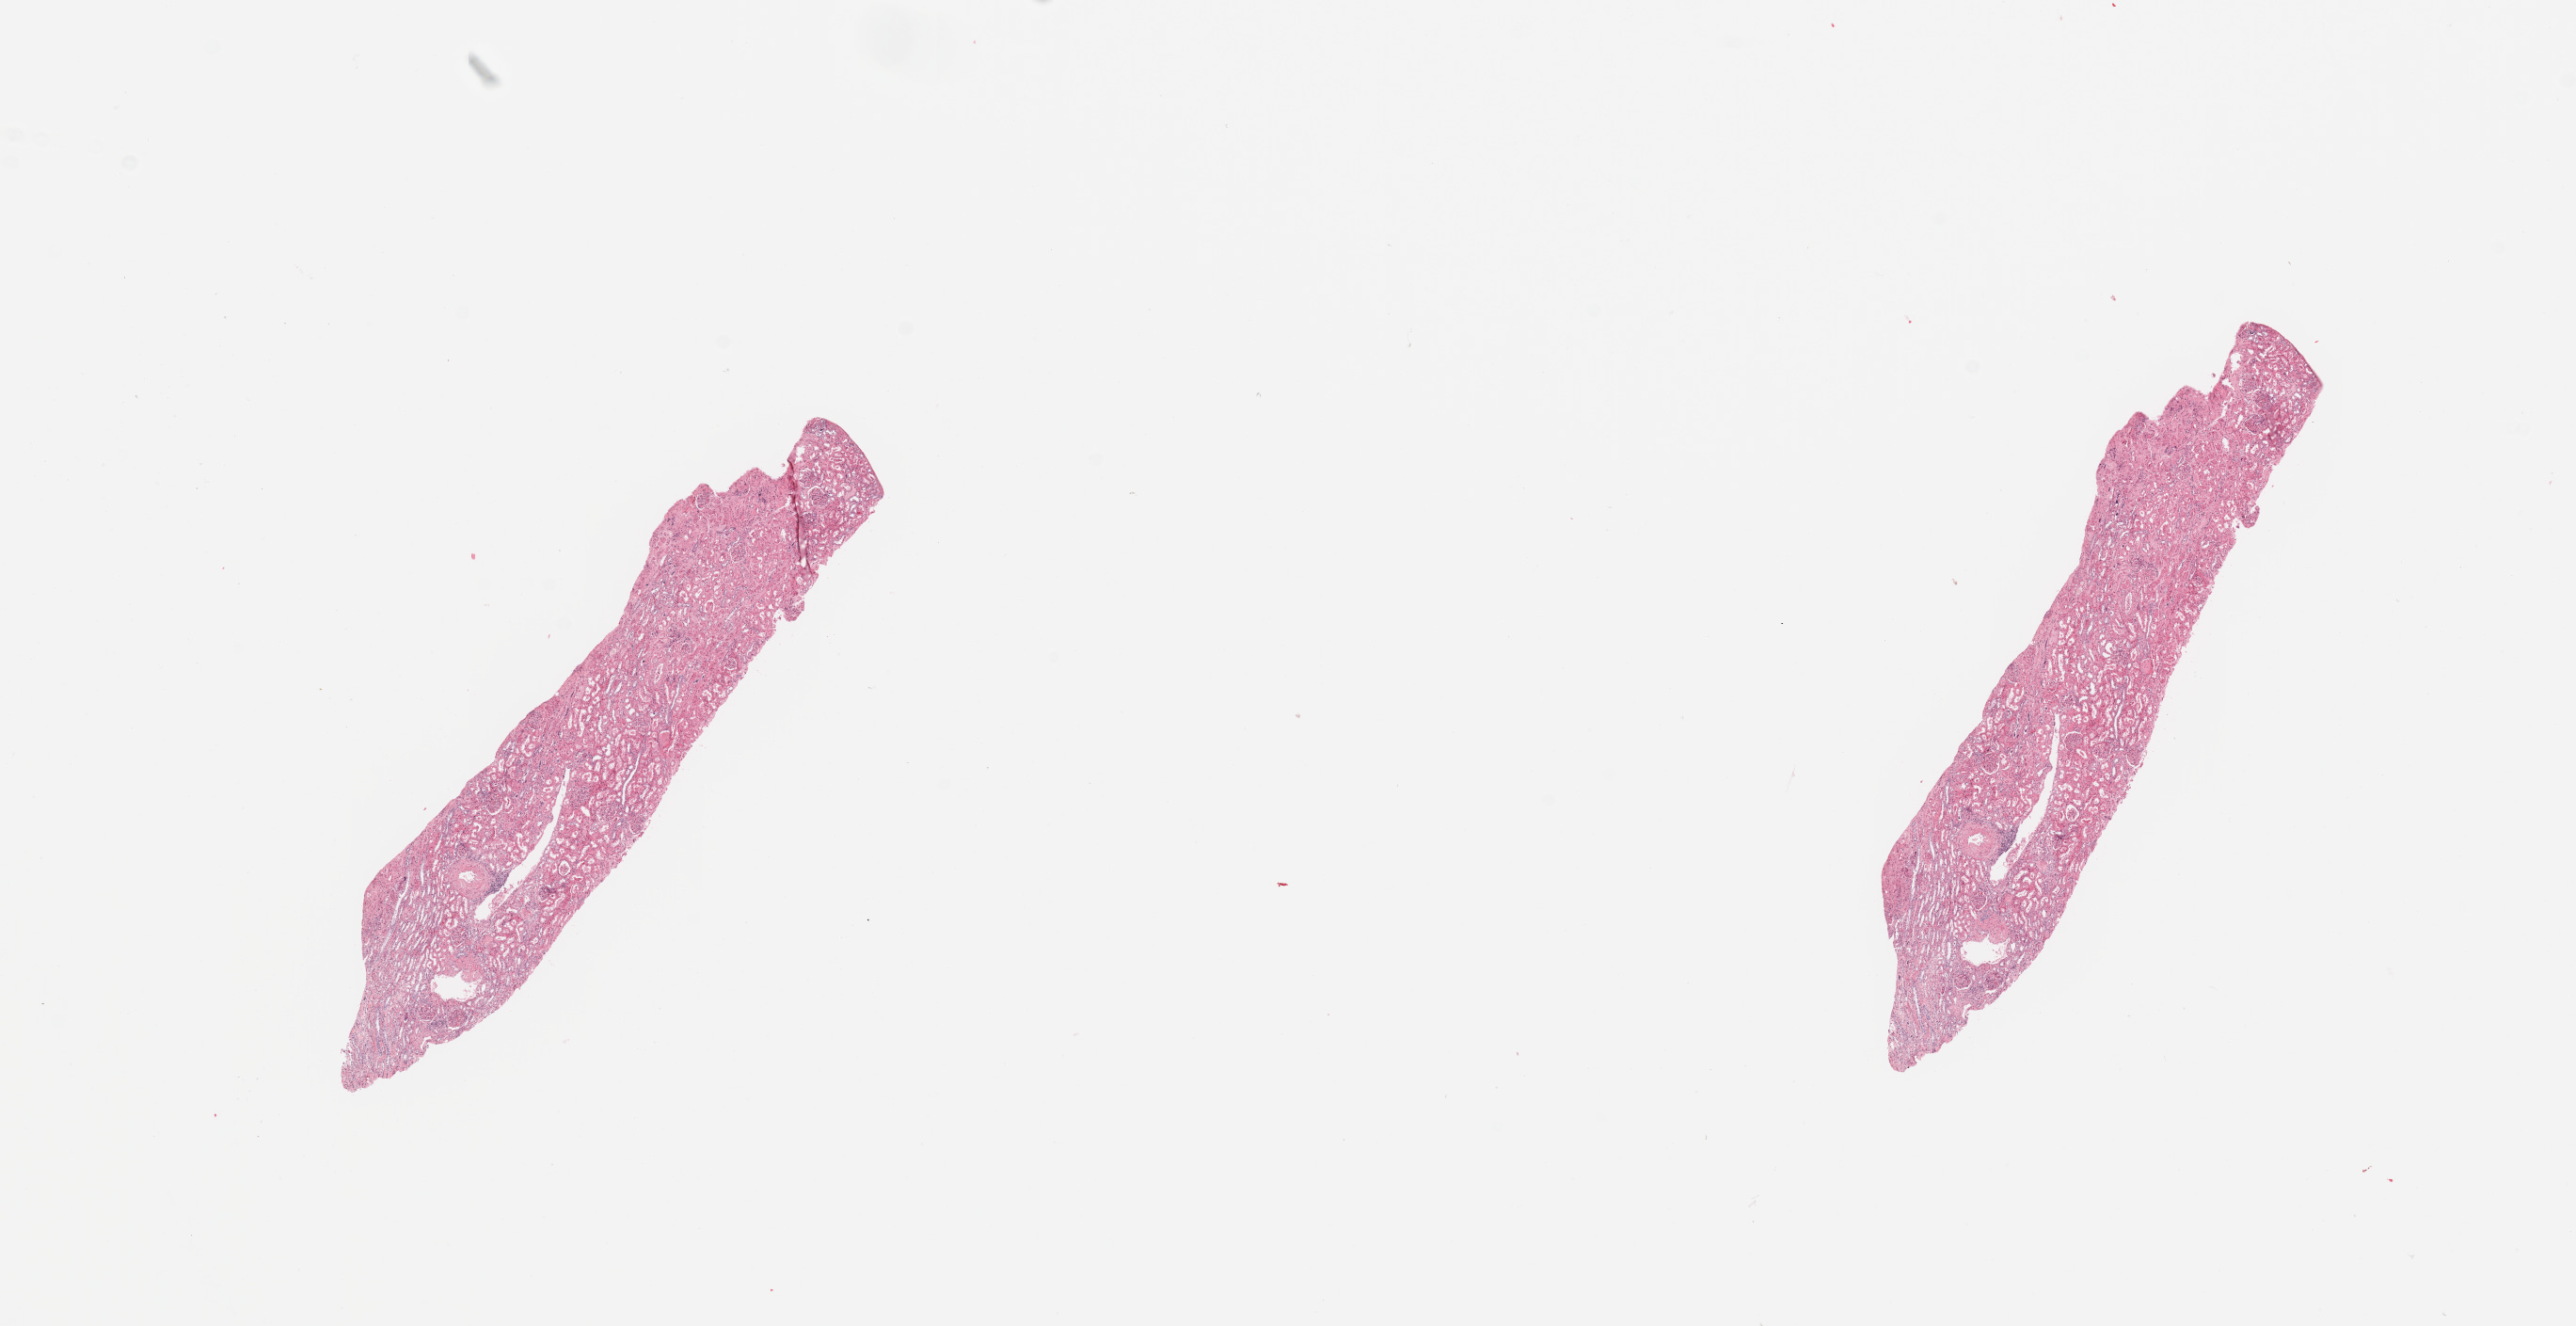
Digitized Hematoxylin and eosin (H&E) stained tissue section (whole slide) — low-resolution overview of the scanned area, about 21.7 x 11.1 mm. Kidney, normal (non-tumour) tissue. Male, 44 y/o.
This section: normal (non-tumour) tissue from the same patient. Patient diagnosis: Renal cell carcinoma, NOS.